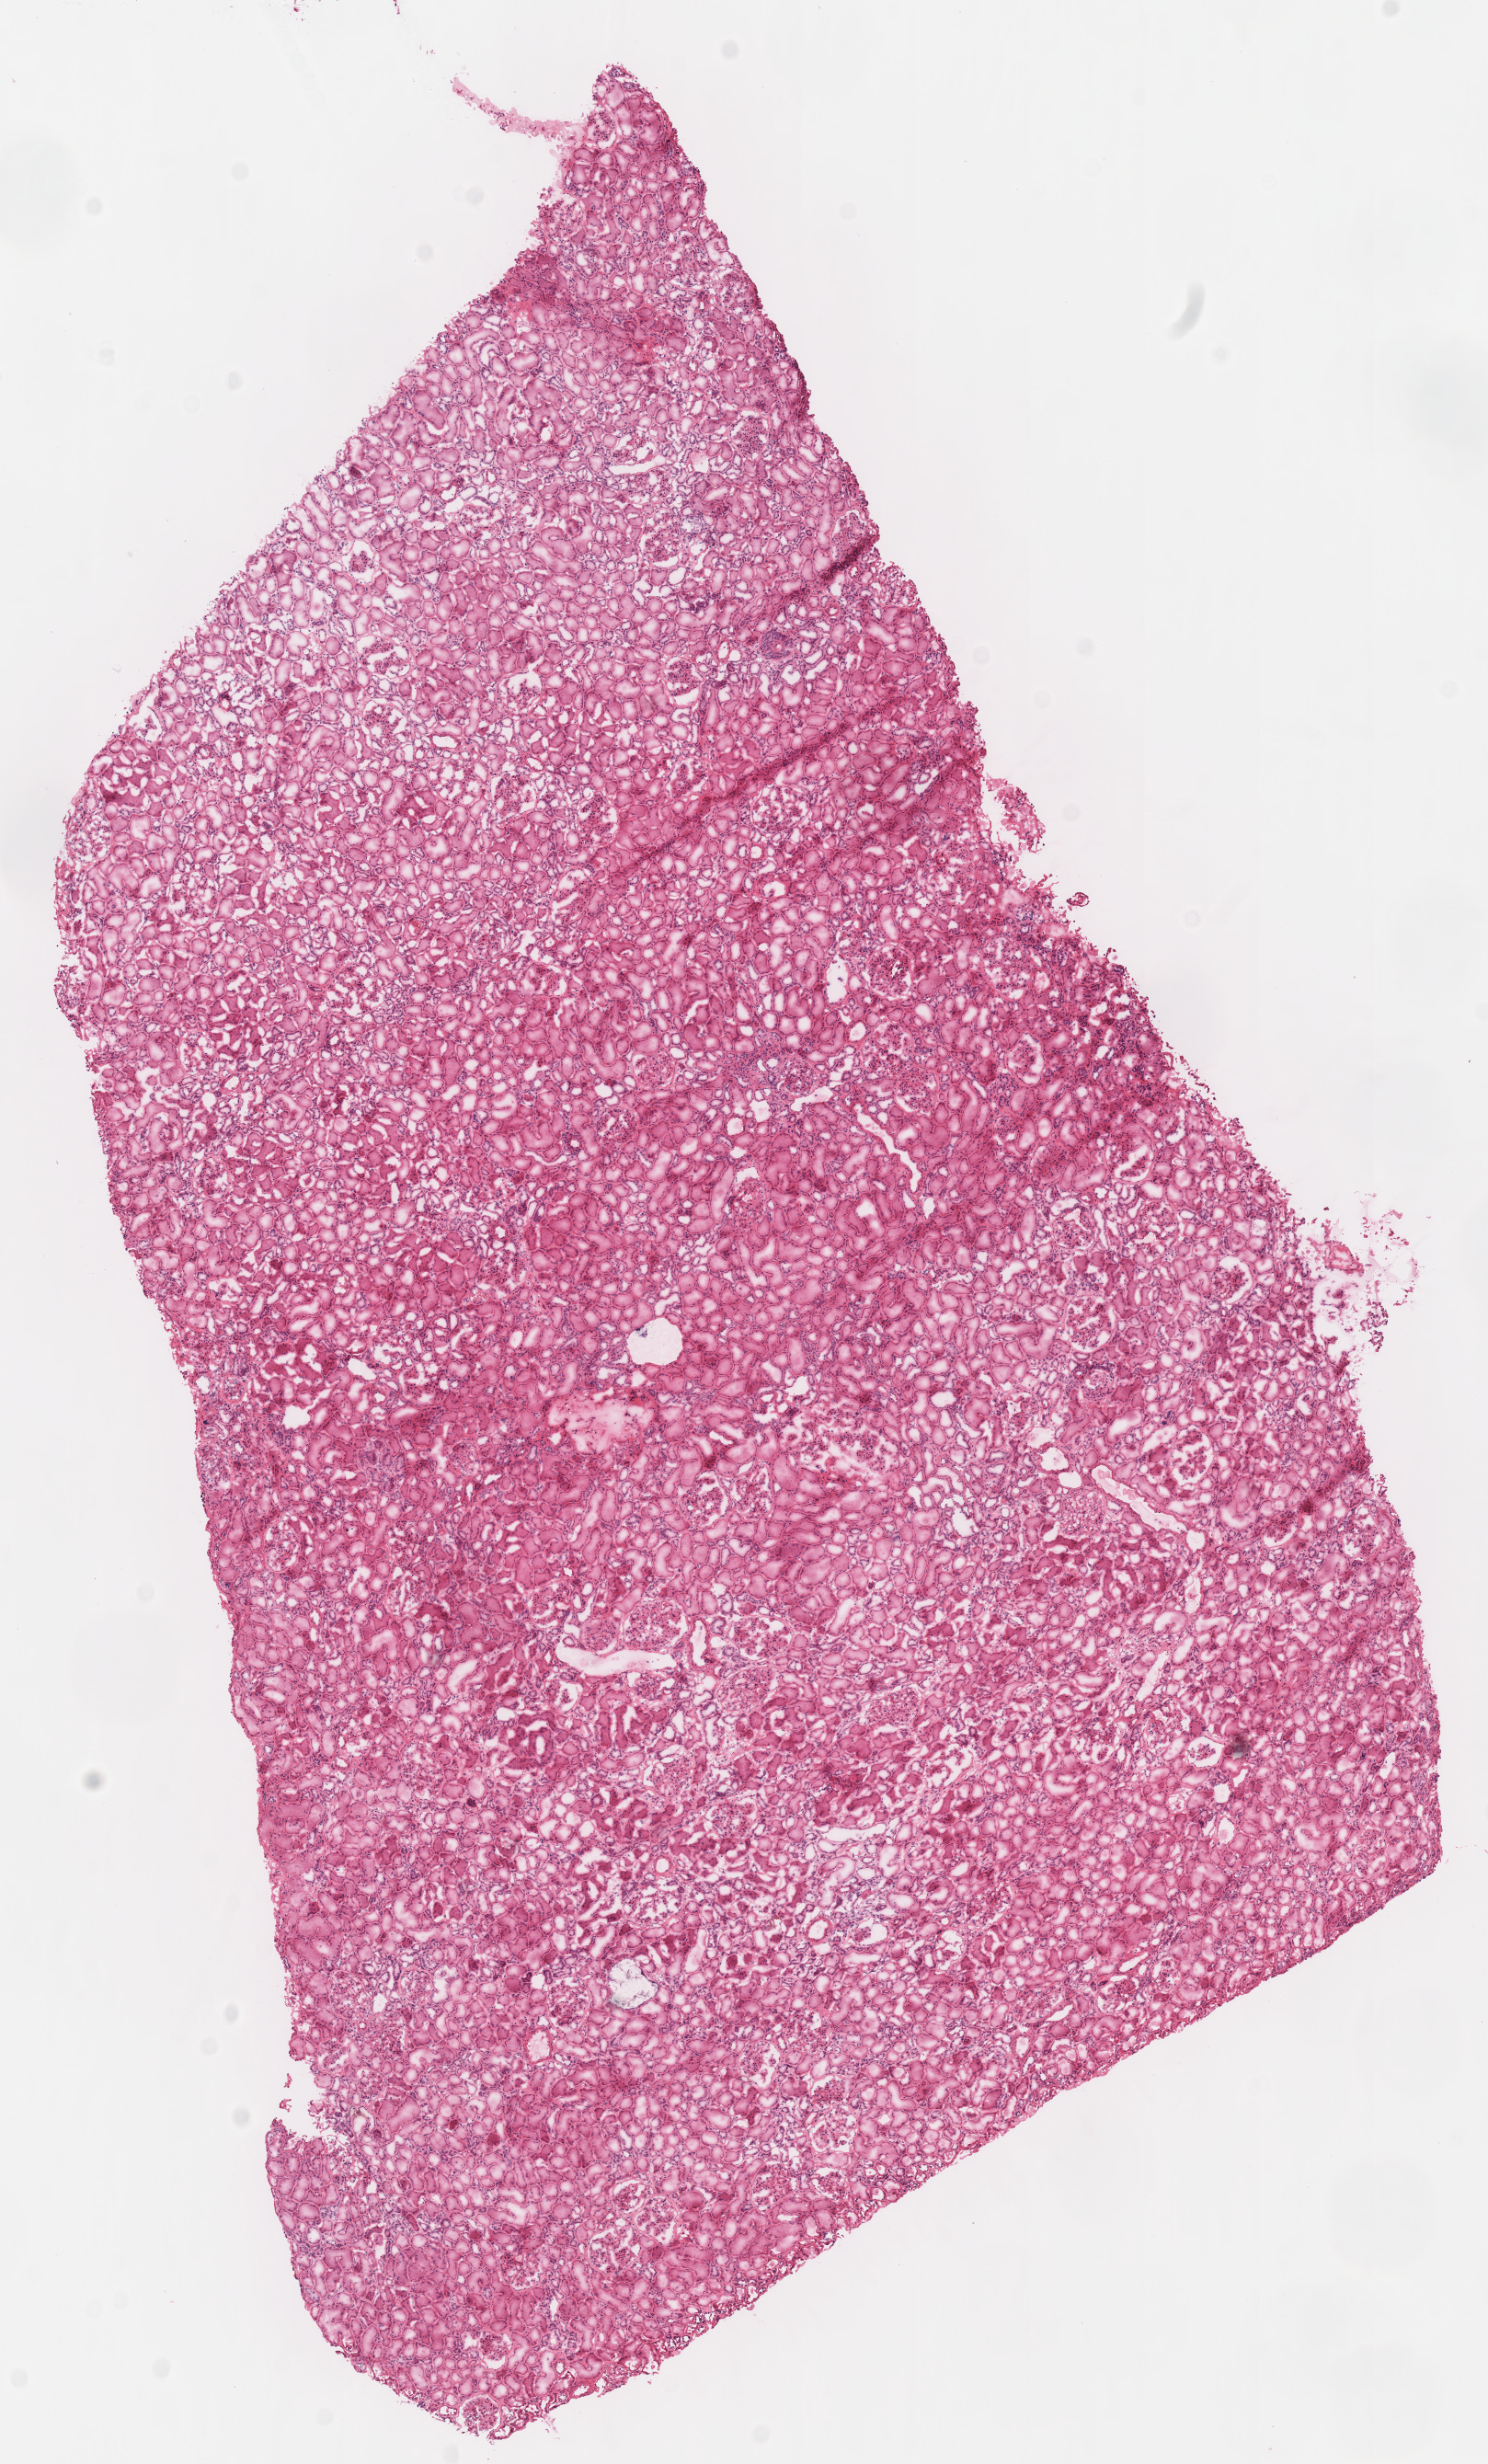
Whole-slide histology image, H&E — a low-resolution overview of the entire scanned area, about 6.4 x 10.5 mm, frozen section, sample: solid tissue normal (non-tumour tissue), kidney. Female, age 57 years at initial diagnosis. Infiltration values recorded for this section: lymphocyte infiltration 0%, monocyte infiltration 0%, neutrophil infiltration 0%.
This section: solid tissue normal (non-tumour) sample from the same patient. Patient diagnosis: Renal cell carcinoma, chromophobe type.